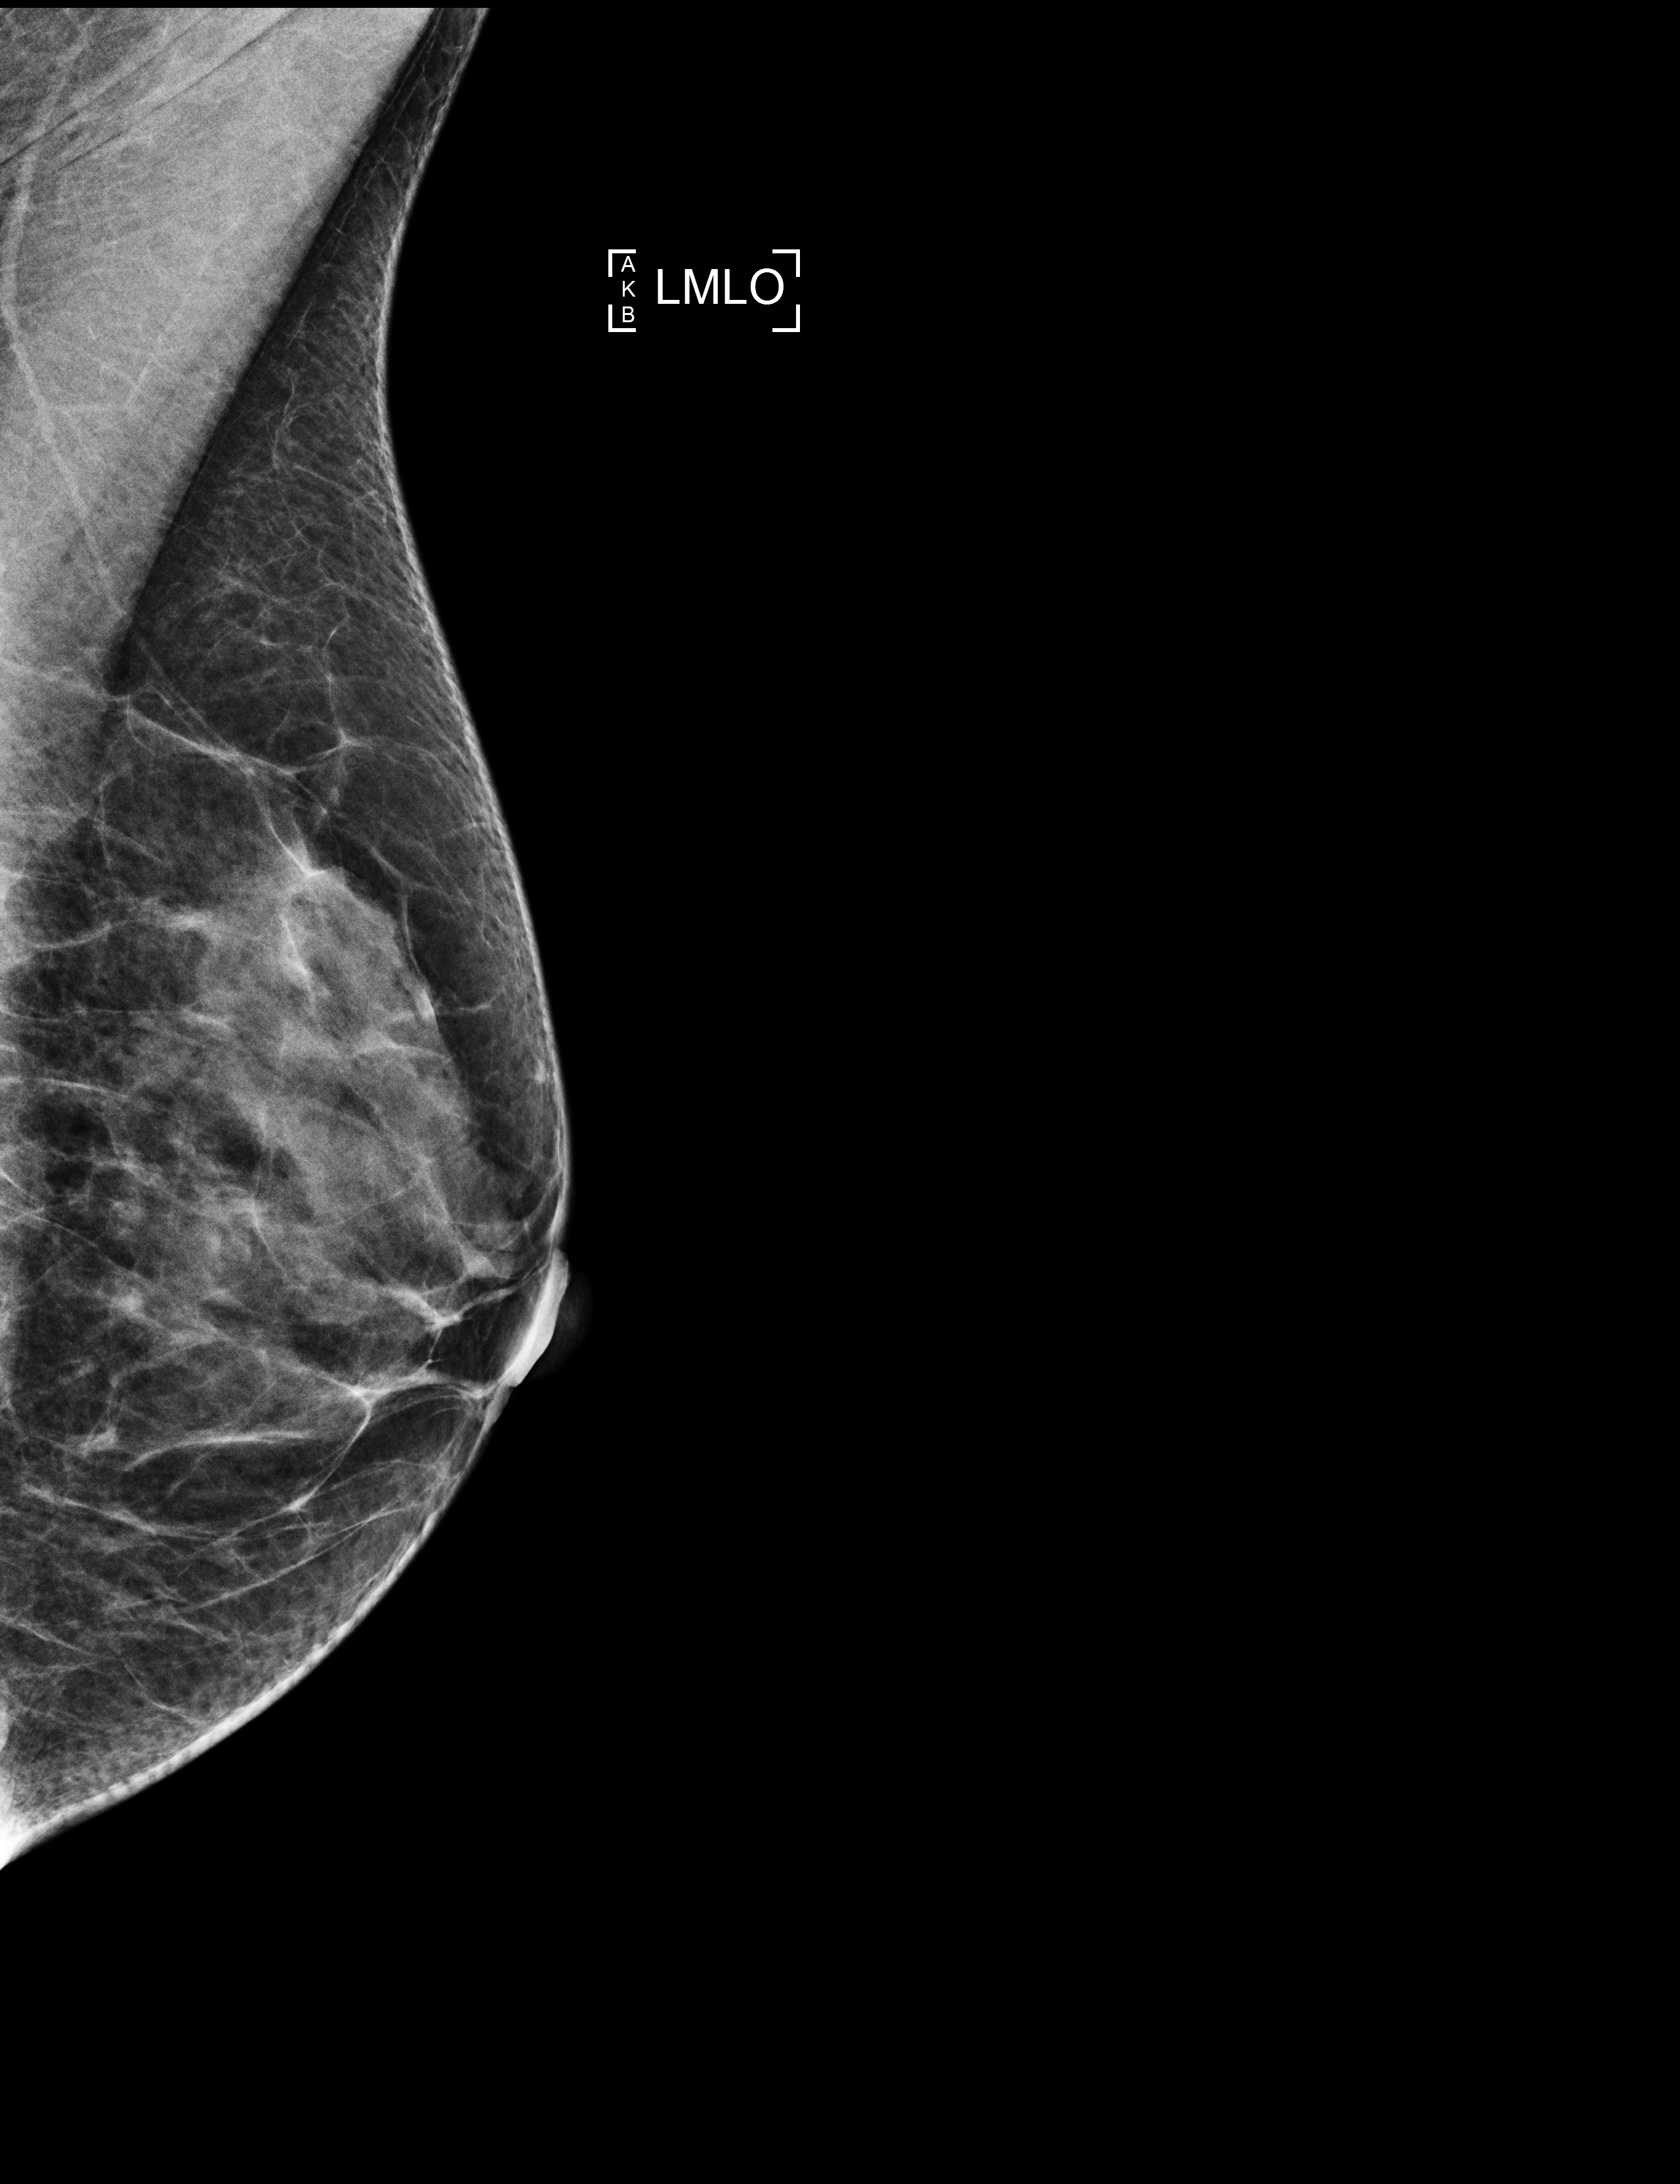
Full-field digital mammogram (FFDM); left breast; MLO view; screening examination; system: Selenia Dimensions. Female patient, age 57 years.
- BI-RADS breast density category at the screening exam (both breasts, scale 1–4): 3
- final BI-RADS category for the screening round (tomosynthesis exam, both breasts): category 1
- recall: no recall after this screen